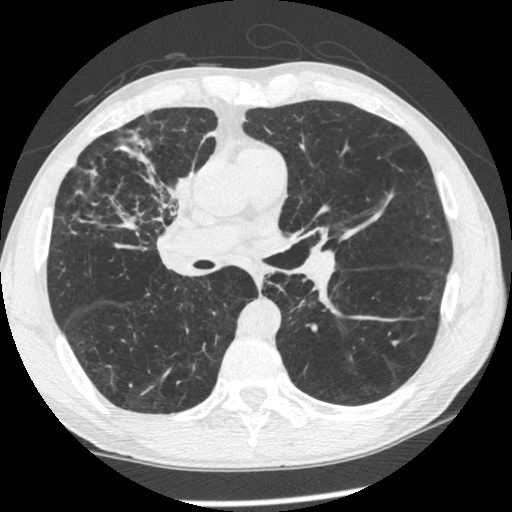
Low-dose screening chest CT, one axial slice. Slice 129 of 261 in the series (ordered by position). Reconstruction kernel STANDARD. 120 kVp. Lung window (W 1500 / L -600 HU). 512 × 512 image matrix, field of view 340 × 340 mm.
Structures marked on this image (manually delineated by an expert):
- lesion 1 (tumor, upper lobe of right lung): bounding box (x1, y1, x2, y2) in pixels: (167, 170, 195, 207)